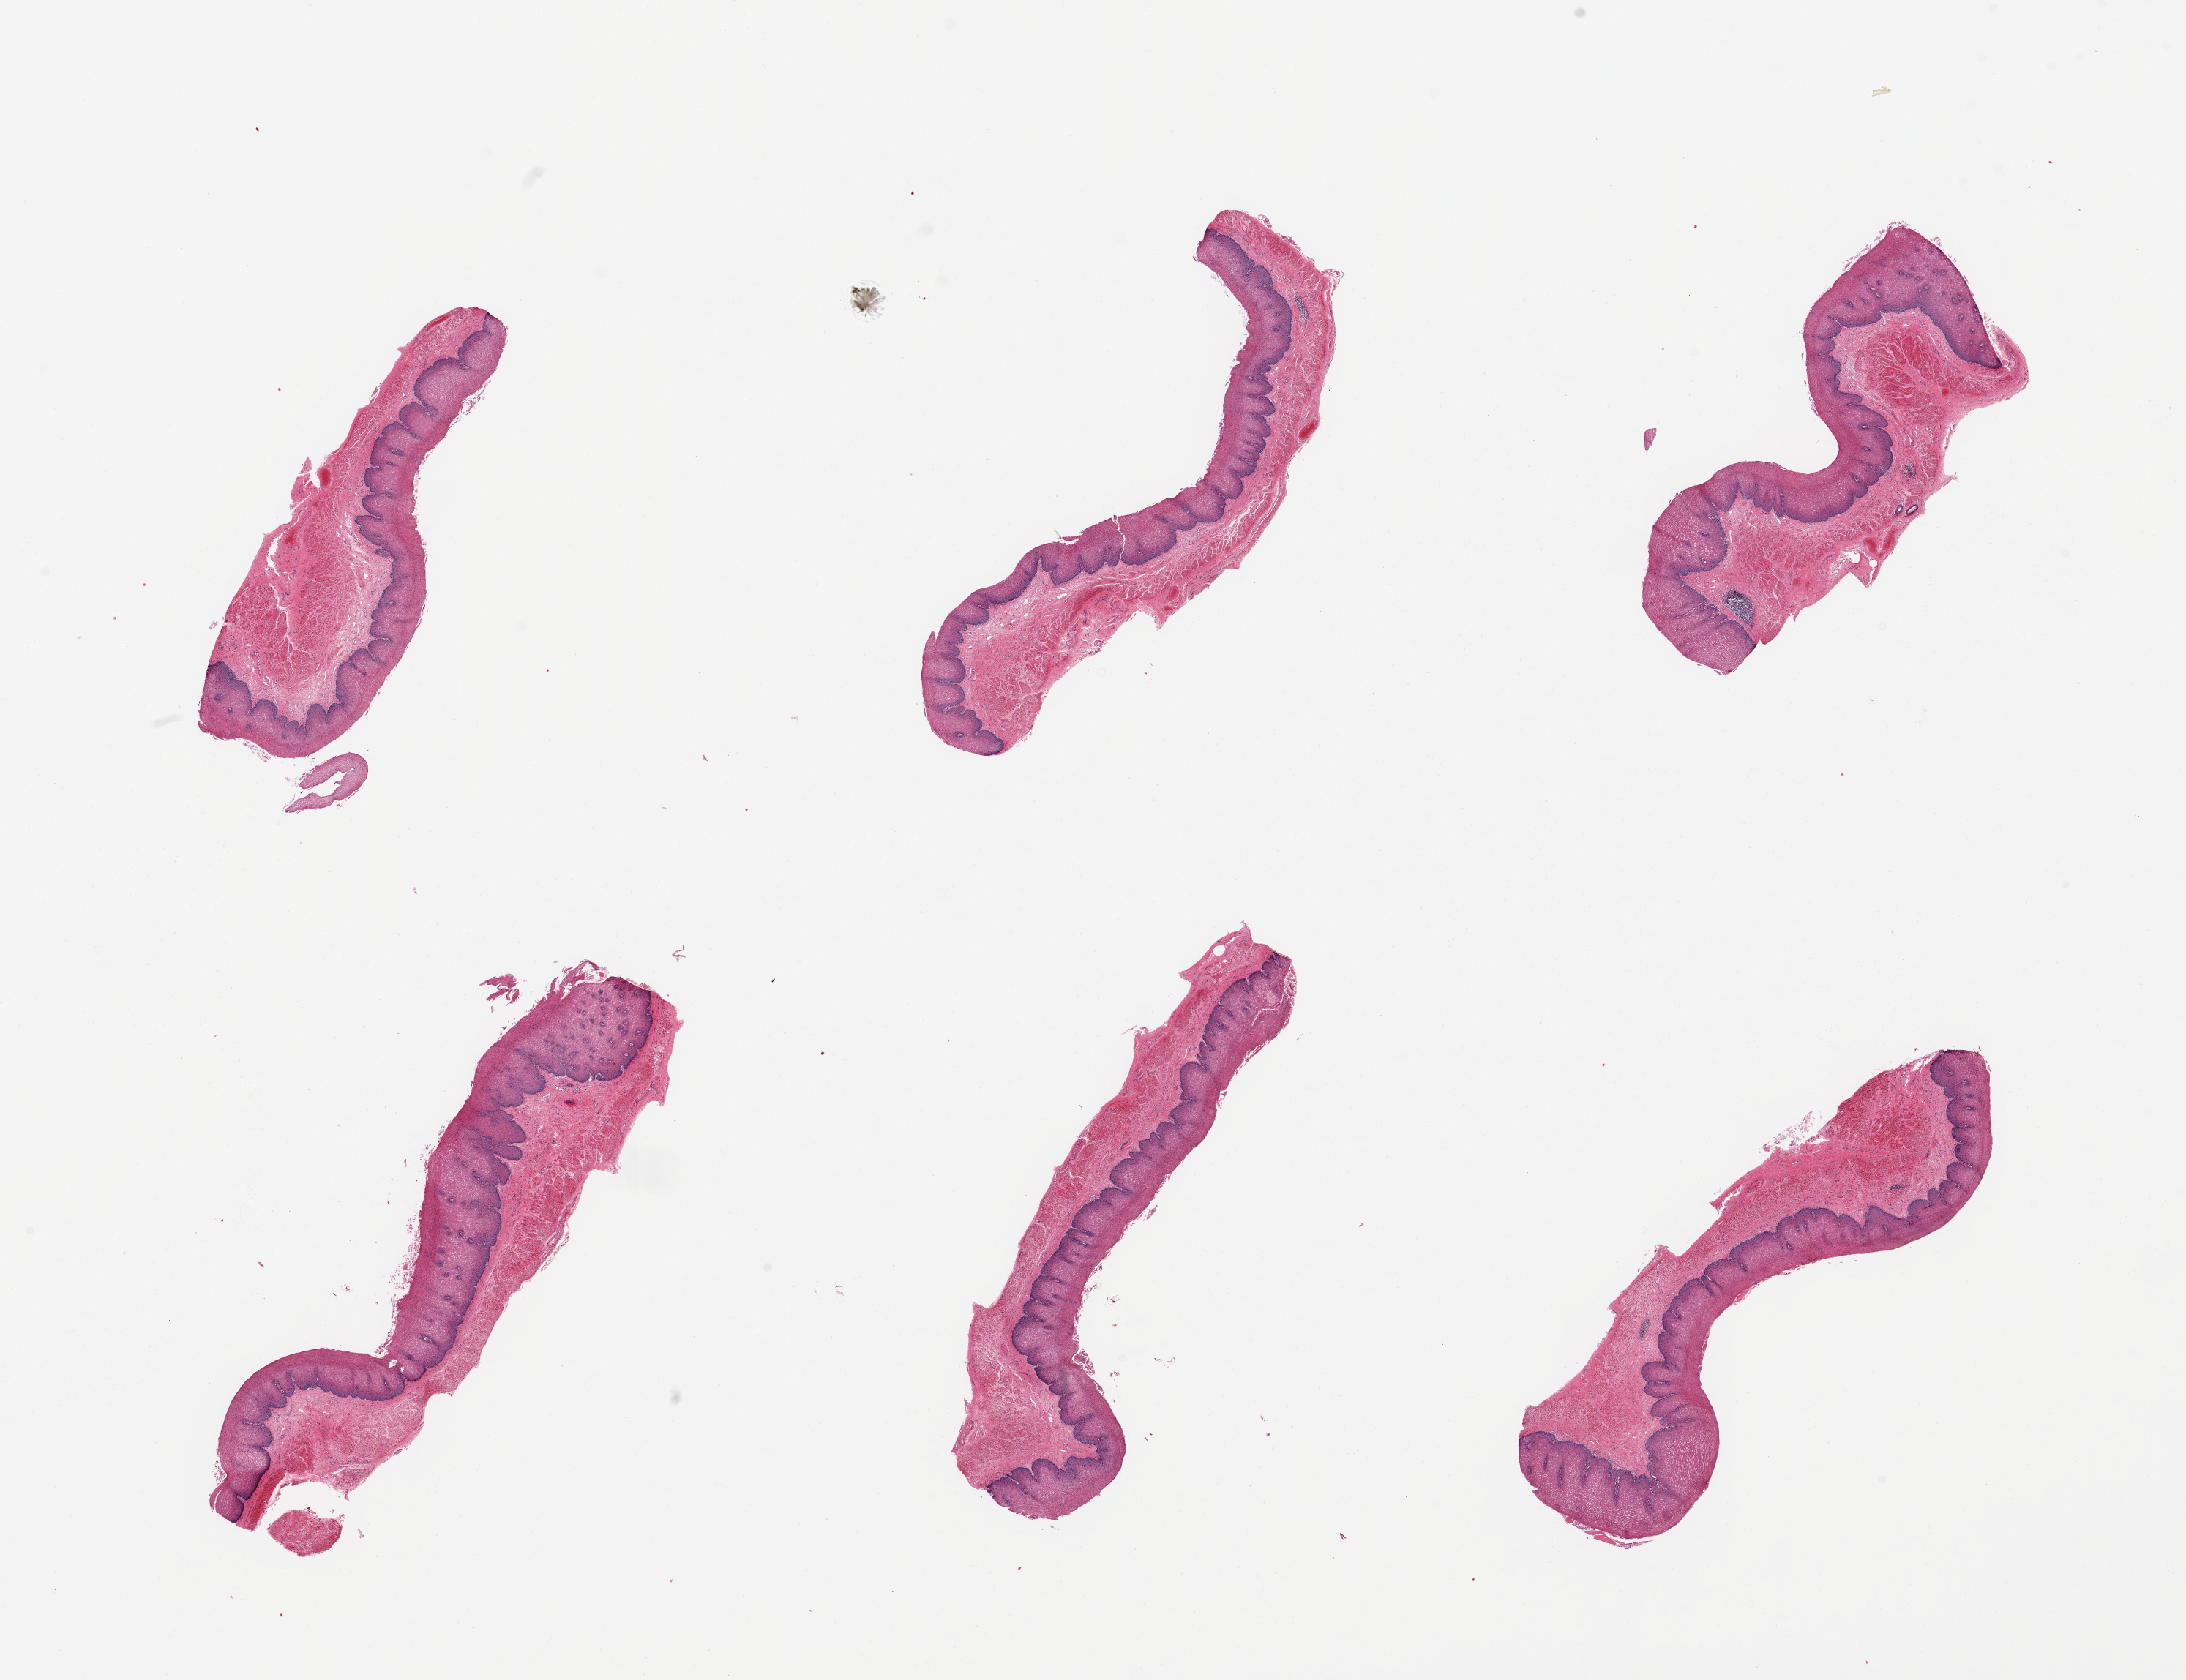
H&E whole-slide image, a low-resolution overview of the entire scanned area, about 23.6 x 18.2 mm. PAXgene-fixed paraffin-embedded (PFPE) section. Sampled site (target tissue): esophageal mucous membrane. Donor tissue sample.
Review note (as recorded): 6 pieces, squamous mucosa up to ~0.5mm, ~50-60% thickness.